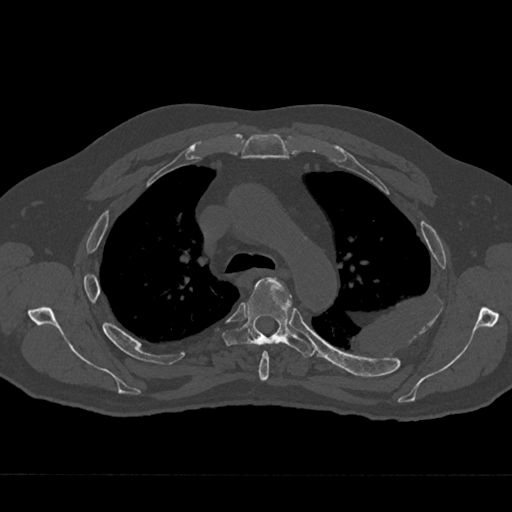
CT including the spine, one axial slice; slice 488 of 797 in the series (ordered by position); reconstruction kernel Br40s/3; 120 kVp; bone window (W 1800 / L 400 HU); 0.5 mm slice thickness; 512 × 512 image matrix, field of view 377 × 377 mm. Male patient, age 75 years. From the clinical record (not read from this slice): primary cancer: renal; vertebrae with lytic lesions (as recorded): T4.
Outlined on this slice (semi-automatically segmented with operator editing):
- T4 vertebra: bounding box [x1, y1, x2, y2] px = [259, 351, 269, 381]
- T5 vertebra: [222, 277, 316, 358]